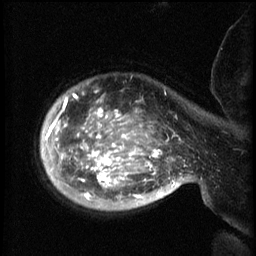
Breast MRI (dynamic contrast-enhanced), one sagittal slice; slice 50 of 60 in the series (ordered by position); 3 images stored at this slice position (order not interpretable as contrast timing); 1.5 T; TE 4.2 ms, TR 8.2 ms; 2.3 mm slice thickness; 256 × 256 image matrix, field of view 200 × 200 mm. Female patient, age 50 years.
Structures marked on this image (semi-automatic segmentation, software-assisted and operator-edited):
- analysis volume of interest (the breast-tissue region the enhancement analysis was run in; not a lesion): box from (x=50, y=82) to (x=169, y=211) px
- tumour enhancement mask (voxels above the 70 % enhancement threshold inside the analysis volume of interest): (x=50, y=94)–(x=167, y=201)